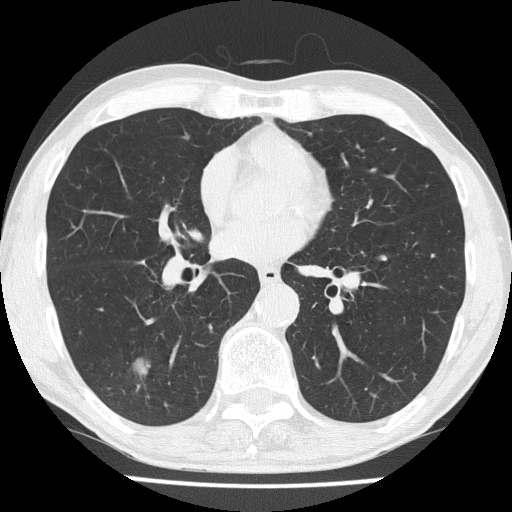
Low-dose screening chest CT, one axial slice; slice 79 of 186 in the series (ordered by position); 120 kVp; lung window (W 1500 / L -600 HU); 2 mm slice thickness; 512 × 512 image matrix, field of view 328 × 328 mm.
Structures marked on this image (manually delineated by an expert):
- lesion 1 (tumor, lower lobe of right lung): bounding box [x1, y1, x2, y2] px = [132, 358, 150, 375]